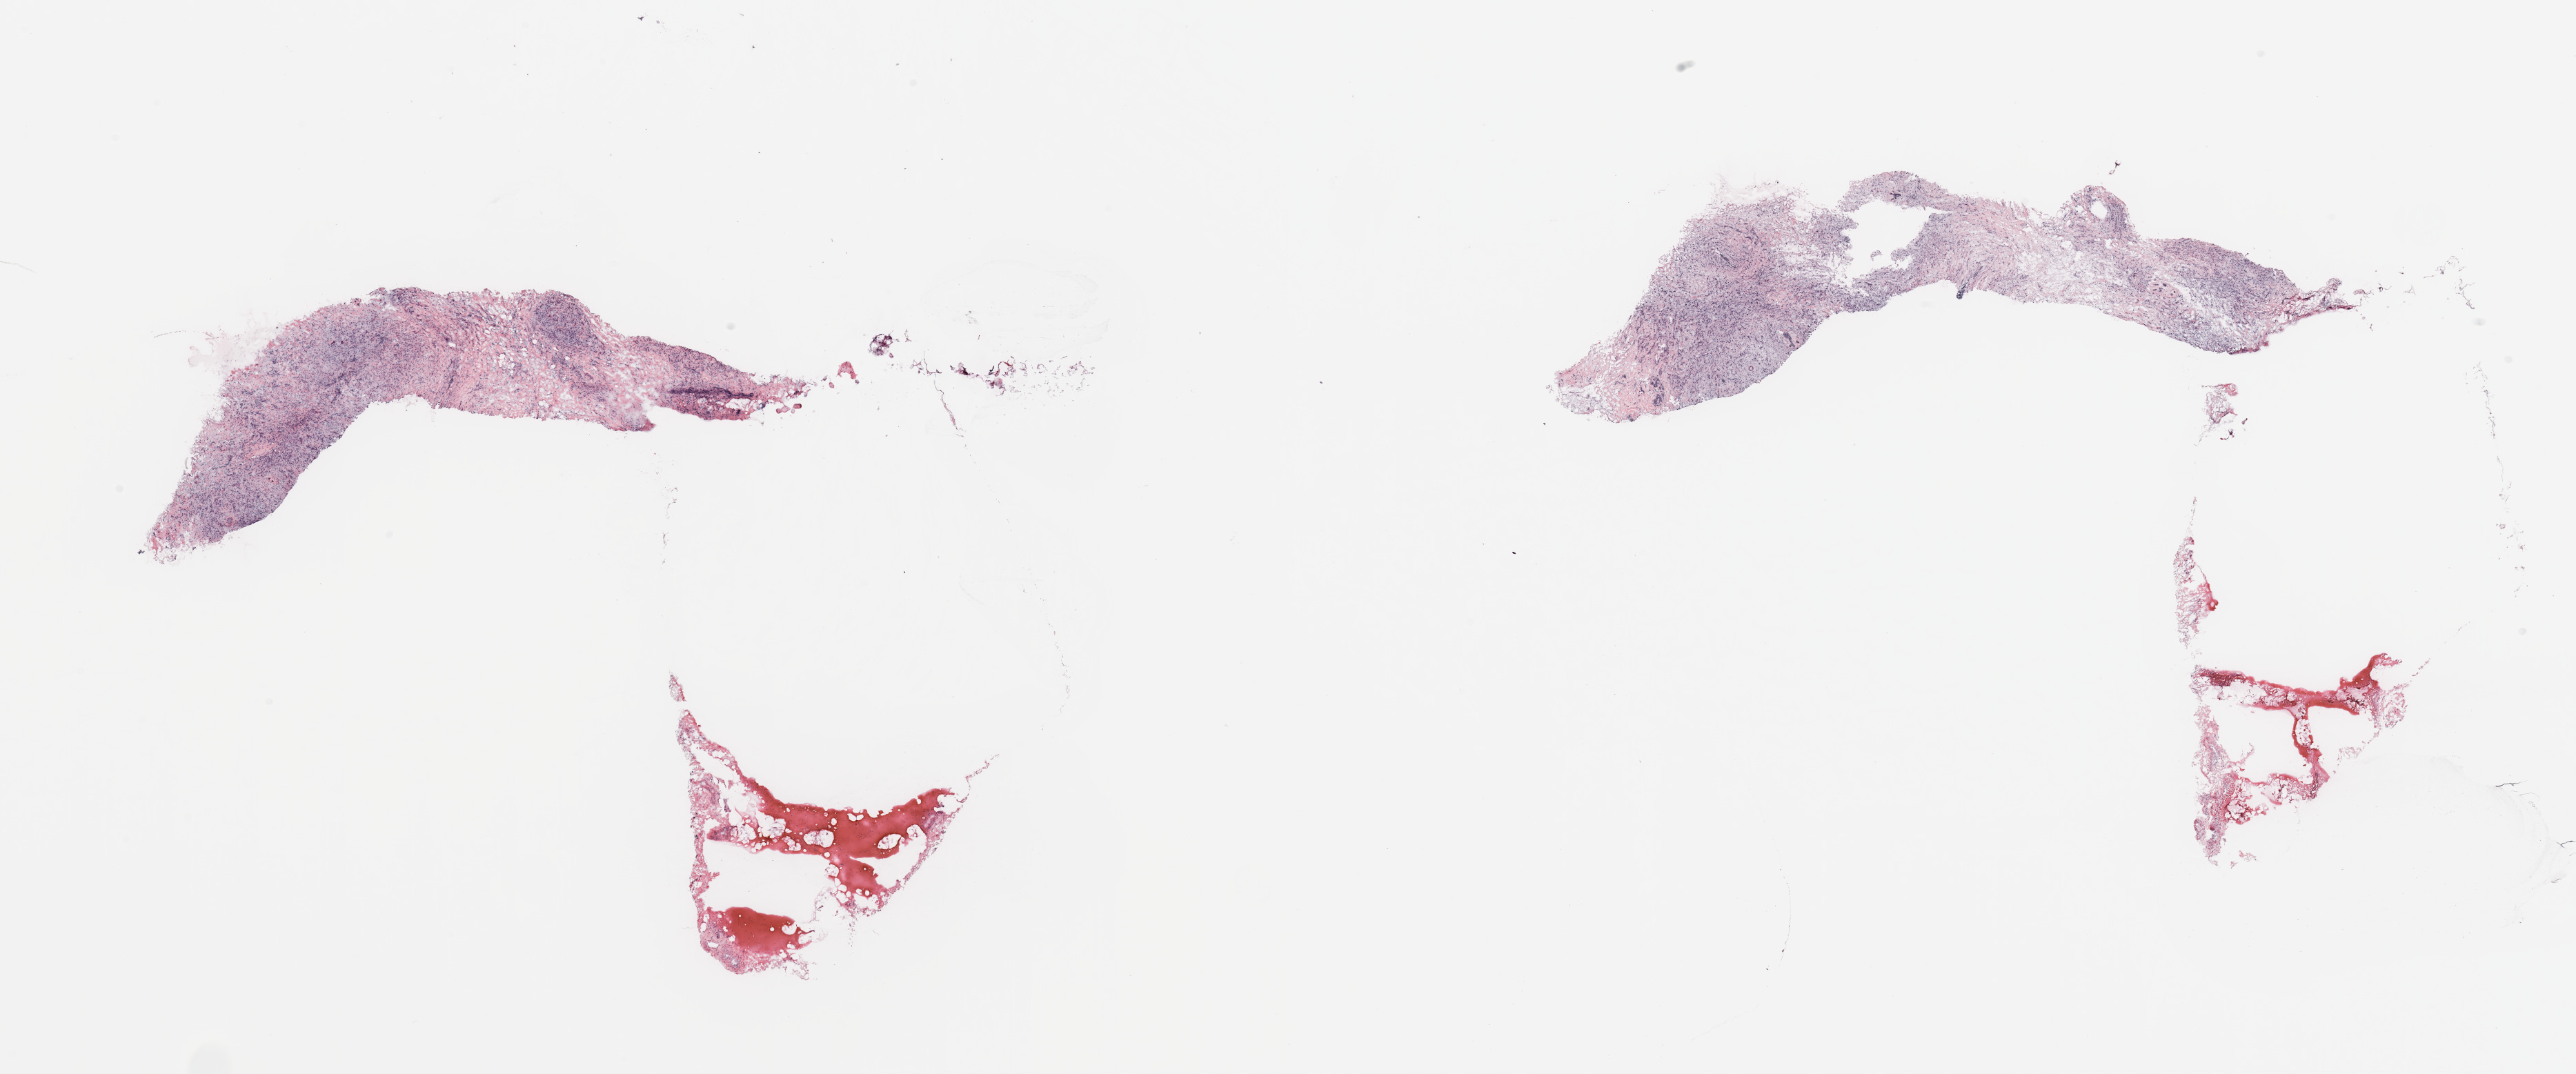
Hematoxylin and eosin (H&E) stained whole-slide image, whole scanned area (about 29.5 x 12.3 mm) shown as a low-resolution overview, breast, tissue type not recorded.
• patient diagnosis (cohort enrolment): breast cancer (breast)